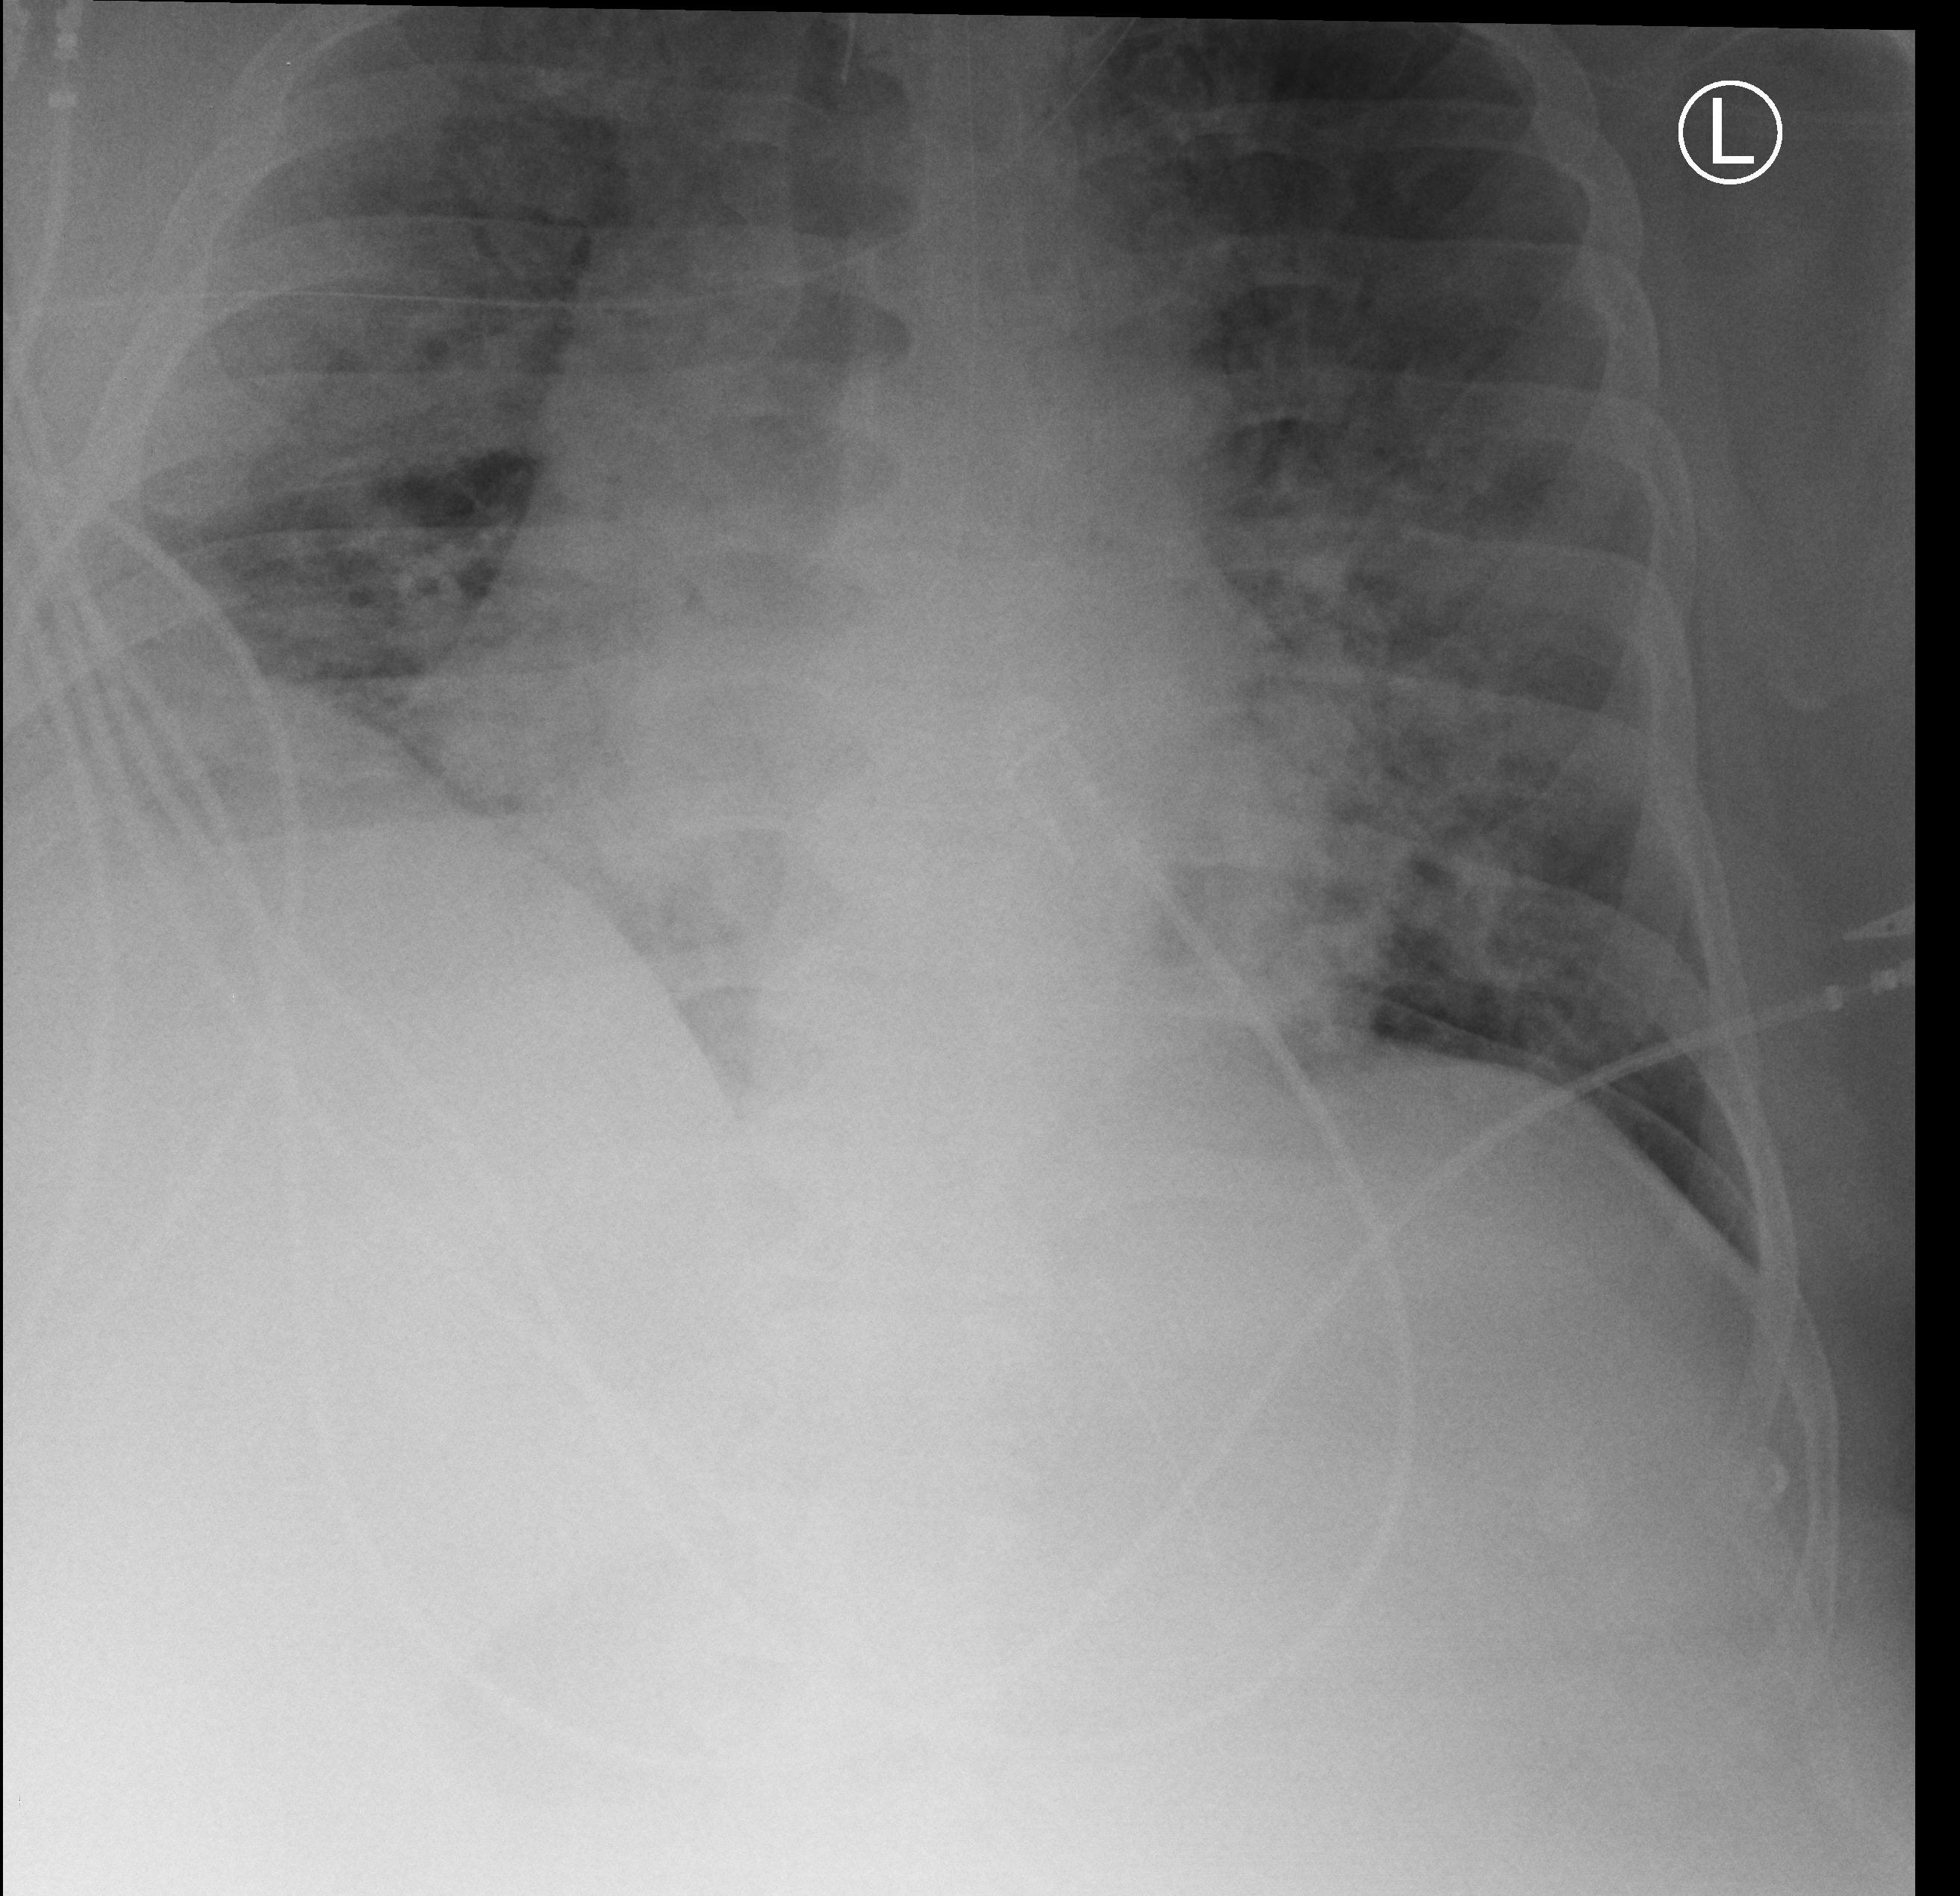
Bedside chest radiograph (computed radiography); anteroposterior (AP) projection. Patient hospitalised with COVID-19; male, aged 18–59 years.
From the hospital-stay record, not from the radiograph (when in the stay this image was taken is not recorded): other chronic lung disease (admission record): yes; admitted to intensive care during this hospital stay: yes; smoking status (admission record): never.